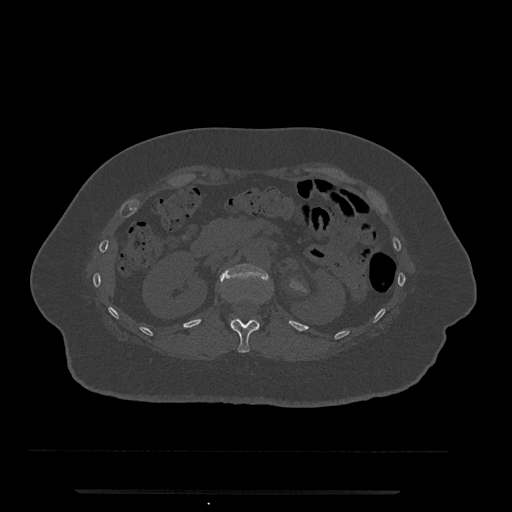
CT including the spine, one axial slice. Slice 142 of 797 in the series (ordered by position). Reconstruction kernel Br40s/3. 120 kVp. Bone window (W 1800 / L 400 HU). 0.5 mm slice thickness. 512 × 512 image matrix, field of view 440 × 440 mm. Female patient, age 51 years. From the clinical record (not read from this slice): primary cancer: neuro.
Structures marked on this image (semi-automatically segmented with operator editing):
- L1 vertebra: box from (x=221, y=264) to (x=269, y=322) px
- T12 vertebra: (x=230, y=318)–(x=259, y=353)